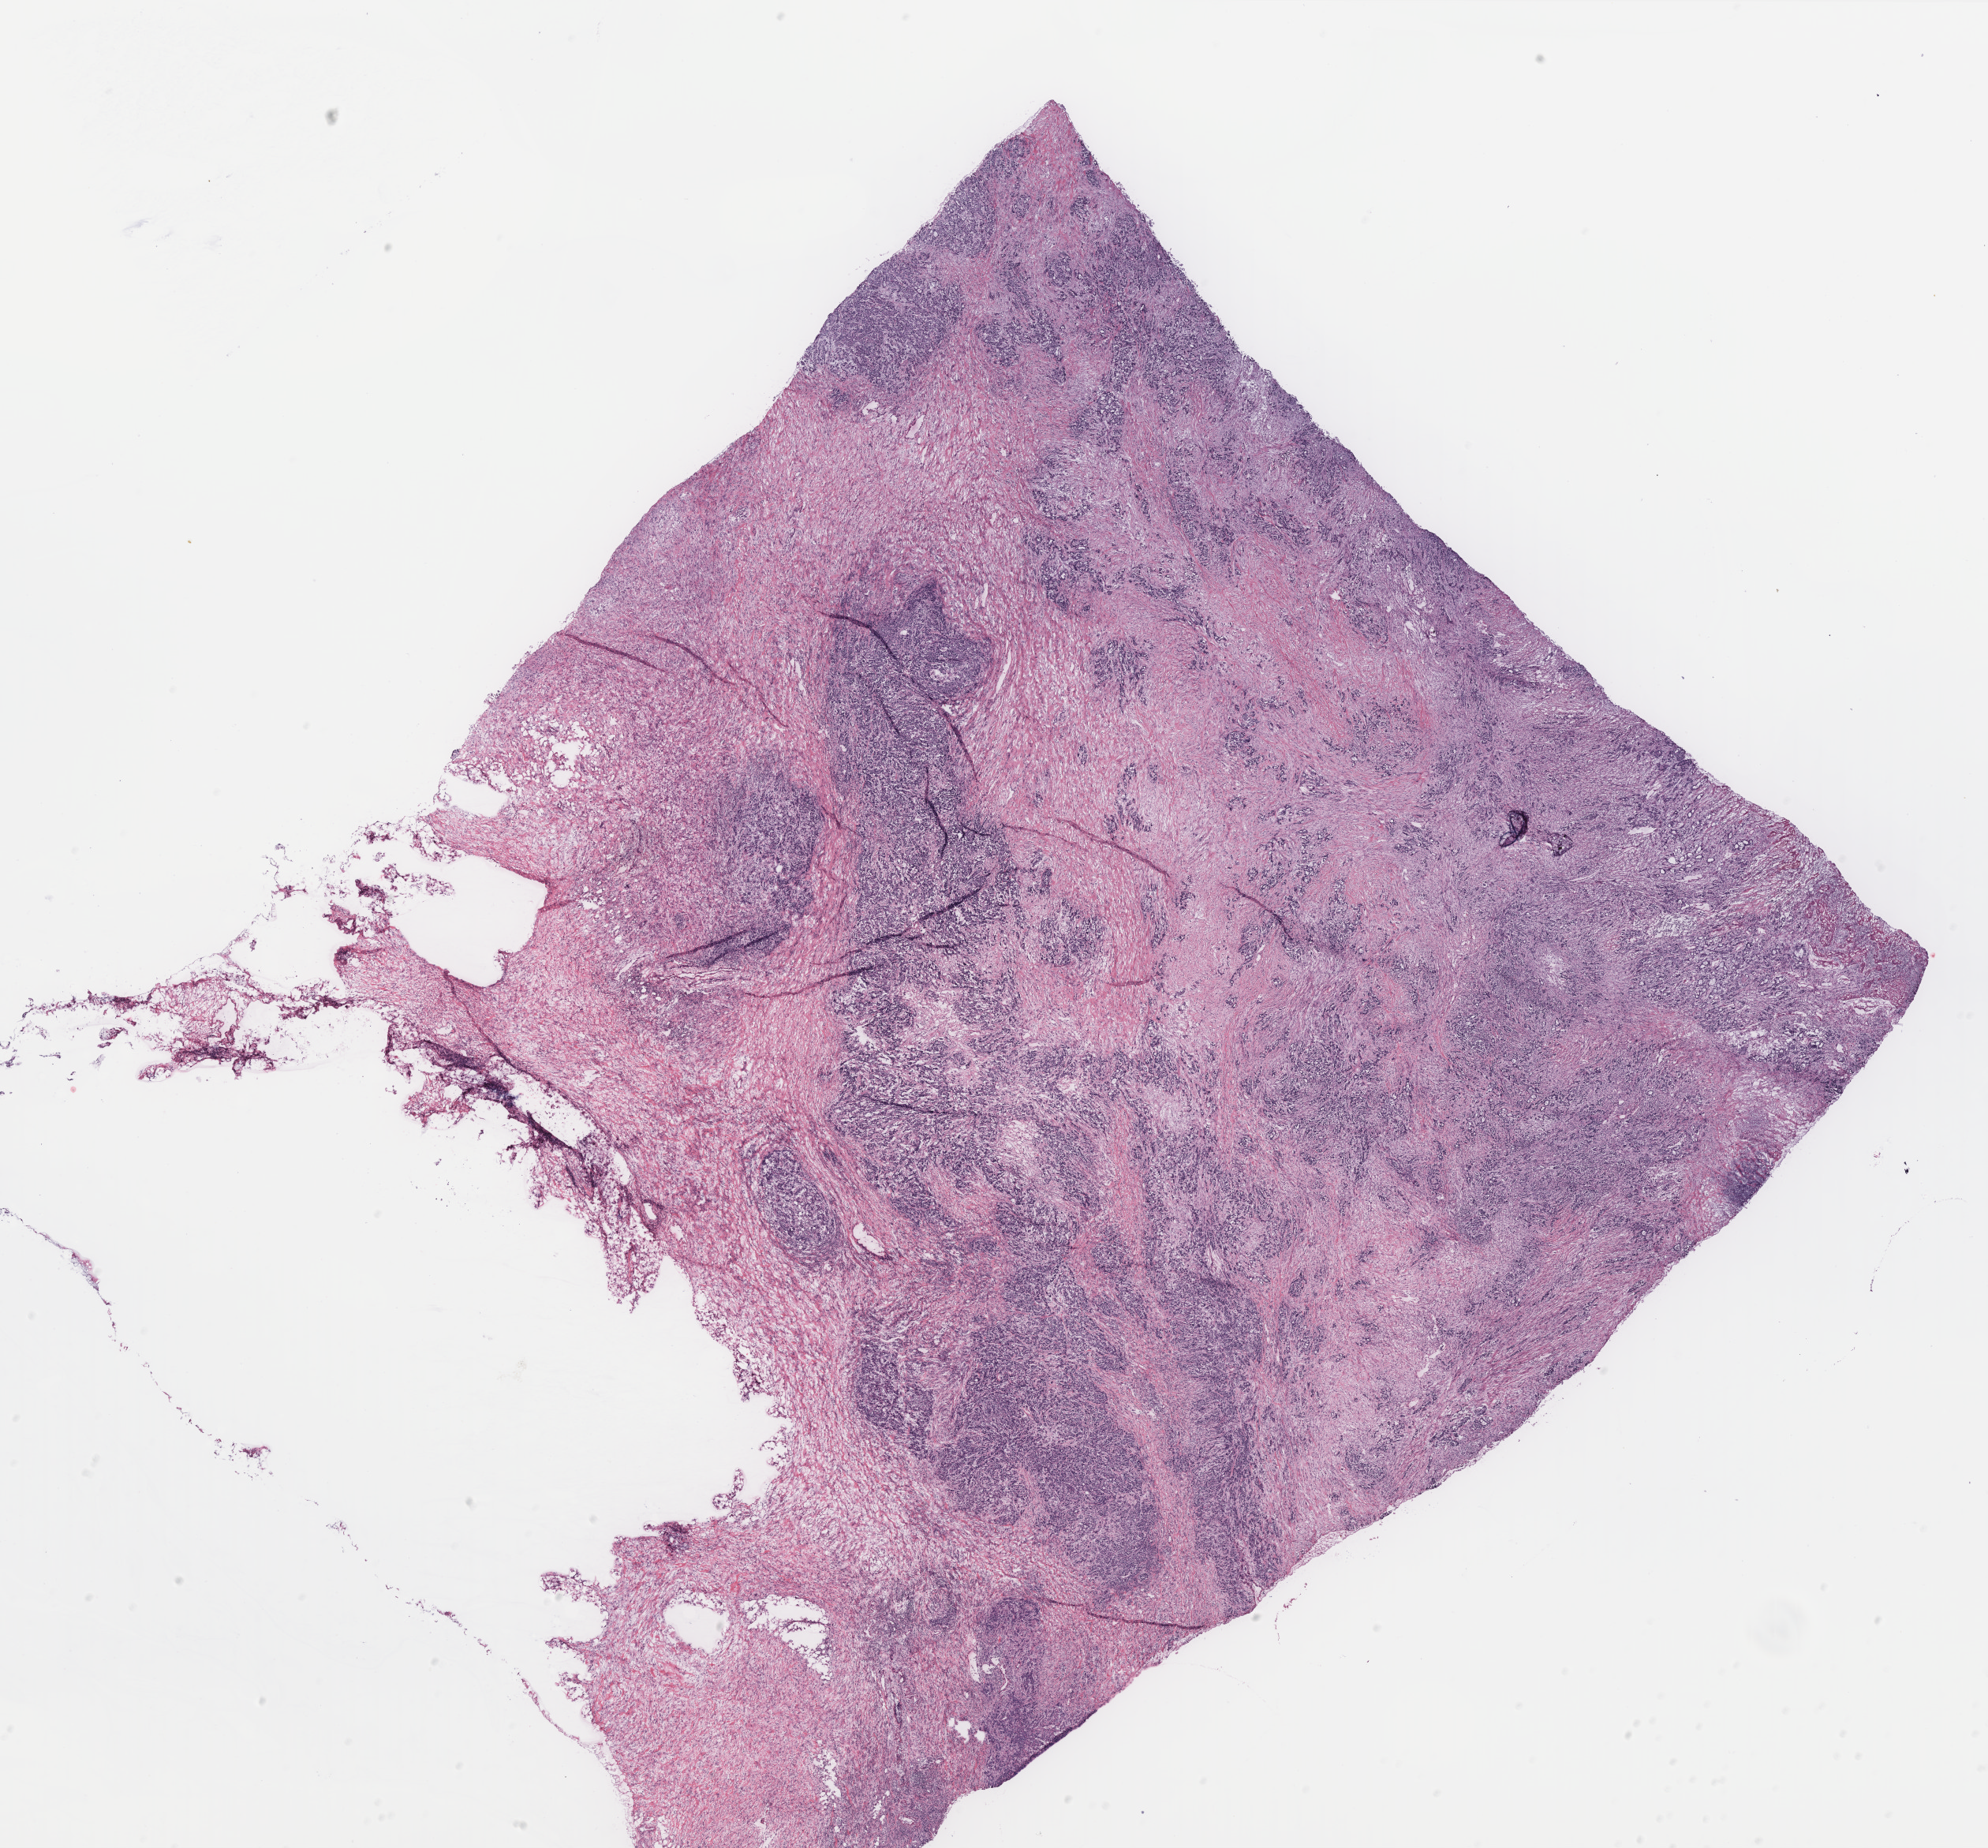
H&E whole-slide image, a low-resolution overview of the entire scanned area, about 20.2 x 18.7 mm, colon, tissue type not recorded.
Patient diagnosis (cohort enrolment): colon cancer (colon).